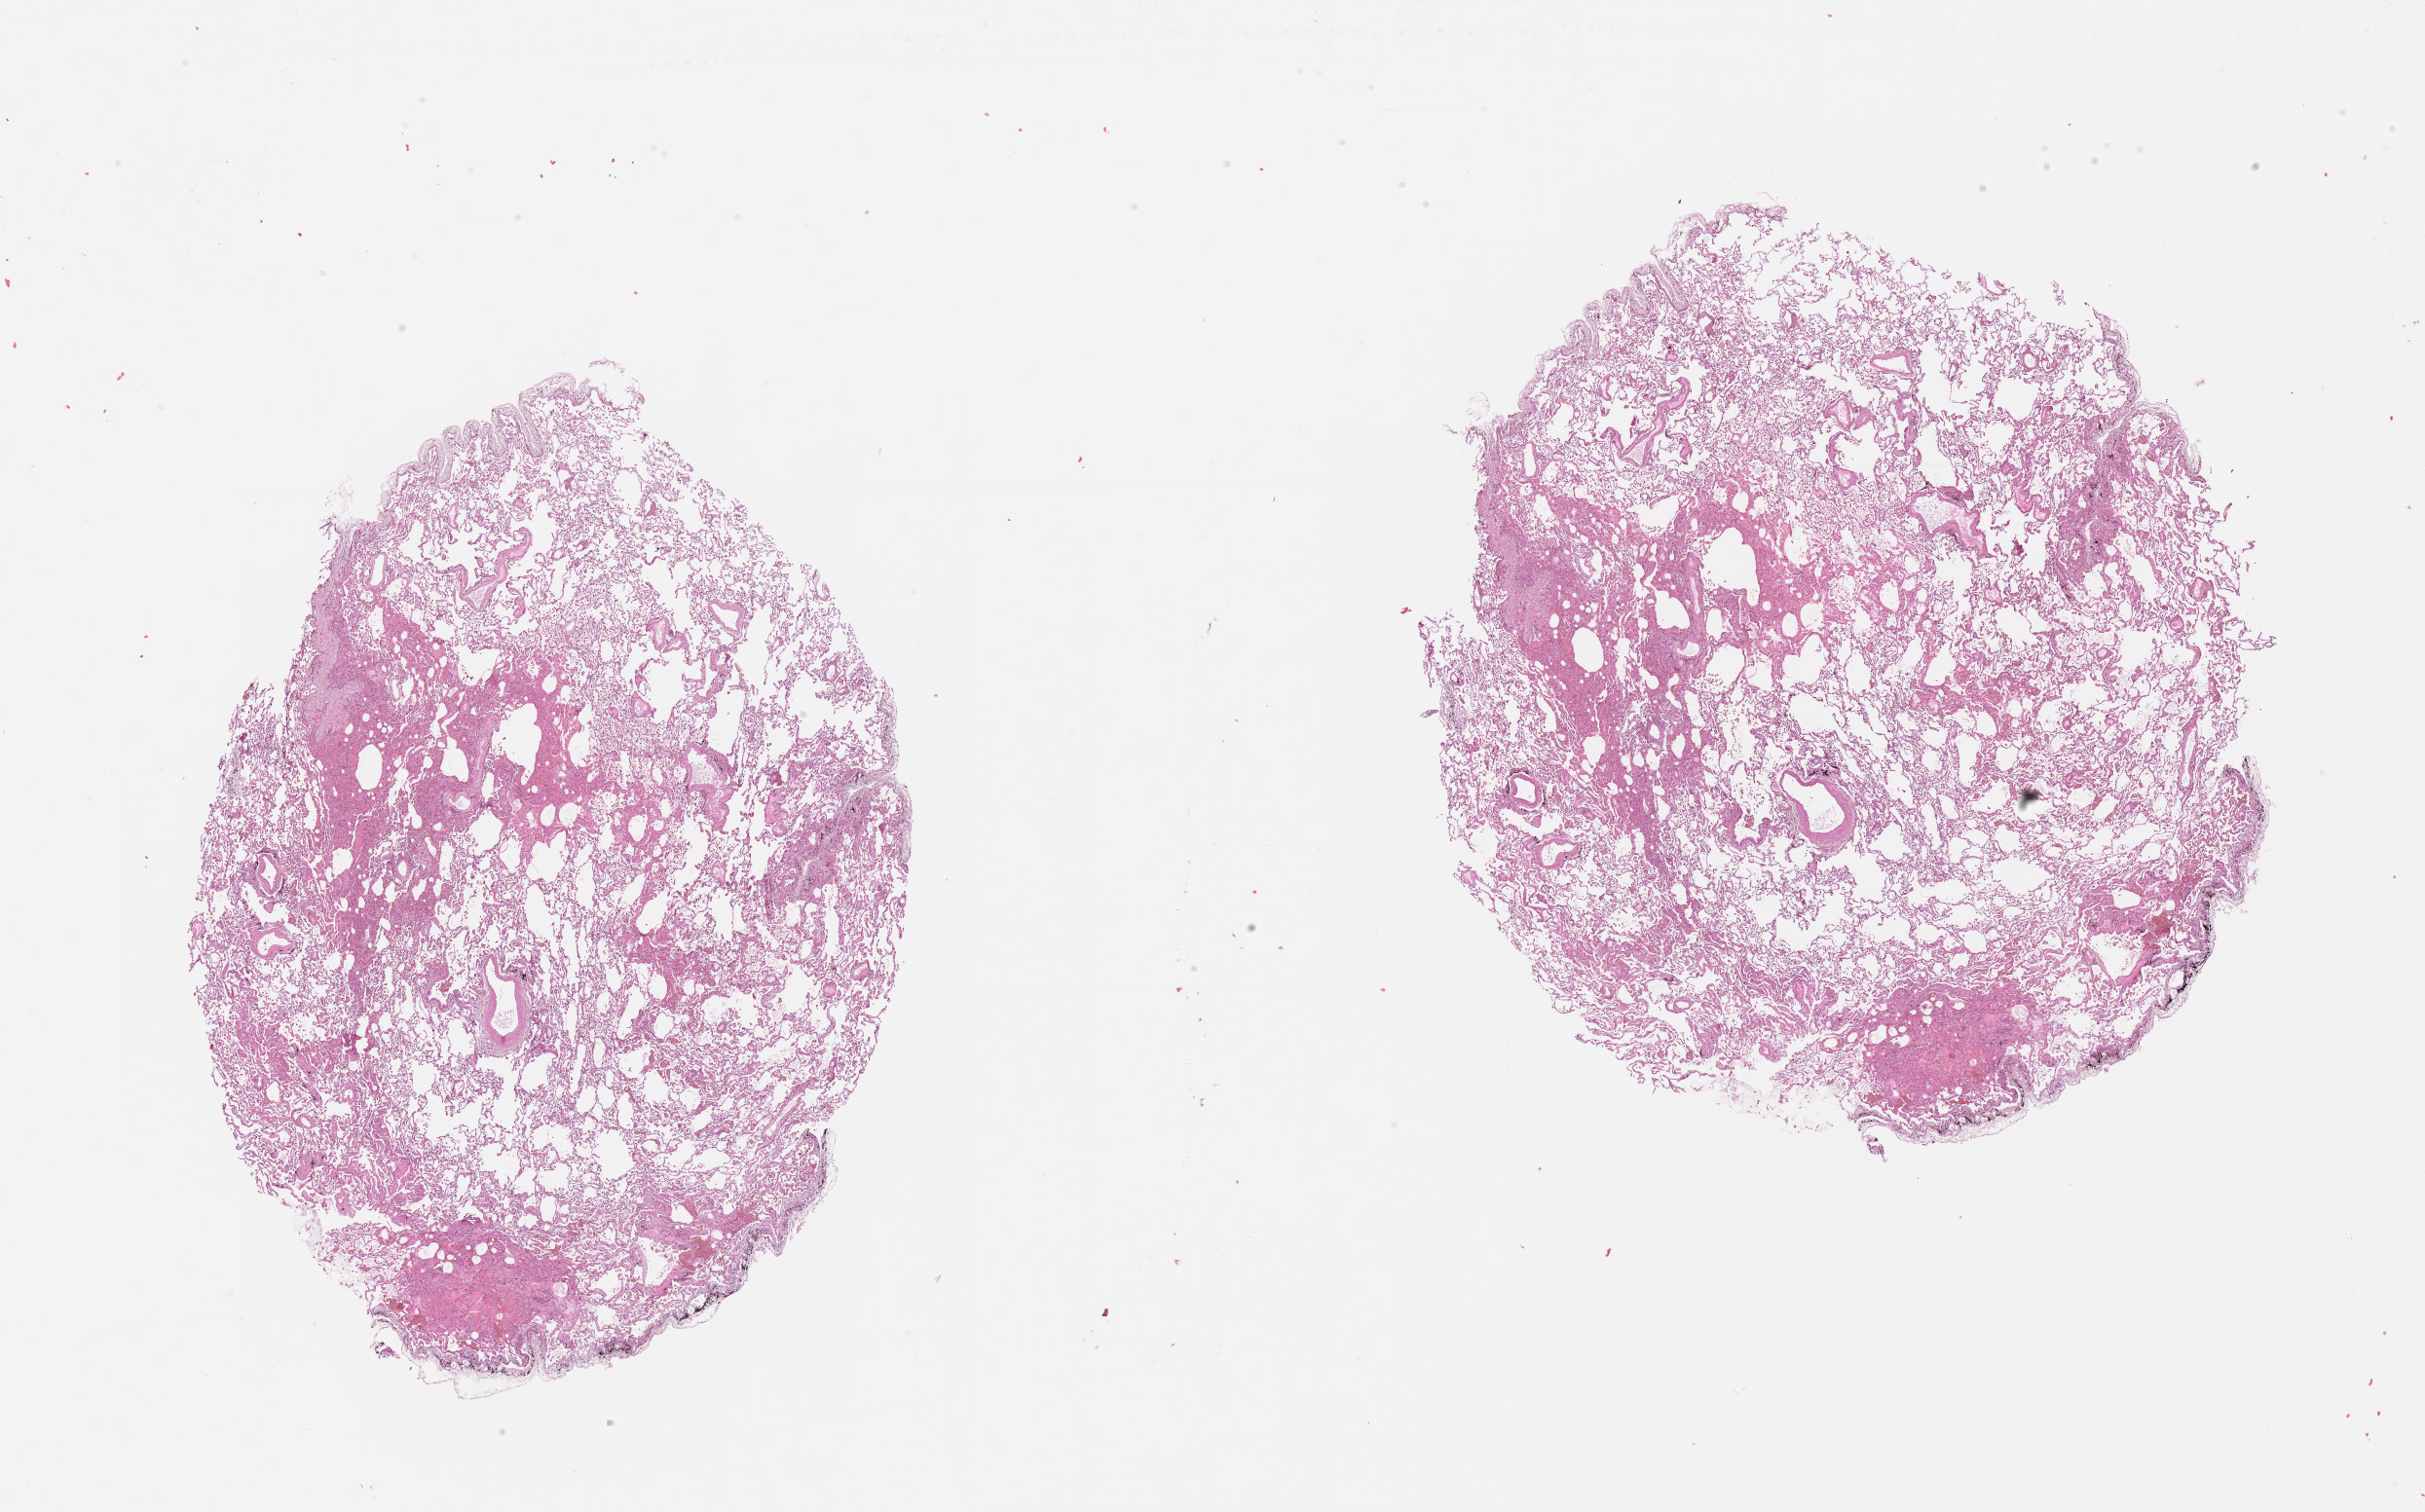
Hematoxylin and eosin (H&E) stained whole-slide image, a low-resolution overview of the entire scanned area, about 20.0 x 12.5 mm; normal (non-tumour) tissue sample, lung. 53-year-old male patient.
- this section: normal (non-tumour) tissue from the same patient
- patient diagnosis (cohort enrolment): squamous cell carcinoma (lung)